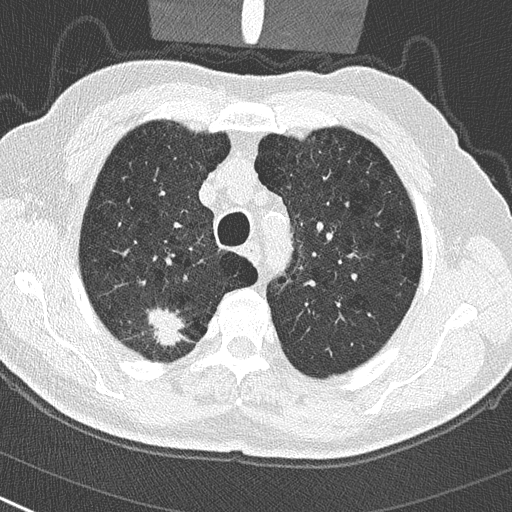
Axial slice from a low-dose chest CT screening exam. First (baseline) screen. Lung window (W 1500 / L -600 HU). 2 mm slice thickness. 120 kVp. Slice 63 of 290 in the series. 512 × 512 image matrix. Male, age 65 years at enrolment.
• Expert reader's lesion annotation, bounding box <132,301,192,356> (left, top, right, bottom; pixels).
• The exam's reader record, not a measurement of the box and not confirmed to be the same lesion: non-calcified nodule or mass ≥4 mm, right upper lobe, 24 × 19 mm, spiculated (stellate) margins, soft tissue attenuation.
• Official screen result: positive, change unspecified: nodule(s) >= 4 mm or enlarging nodule(s), mass(es), or other non-specific abnormalities suspicious for lung cancer.
• Participant outcome: lung cancer diagnosed 32 days after this screen — non-small cell carcinoma, right upper lobe, poorly differentiated (G3), stage IA (AJCC 6th edition), 29 mm at pathology.